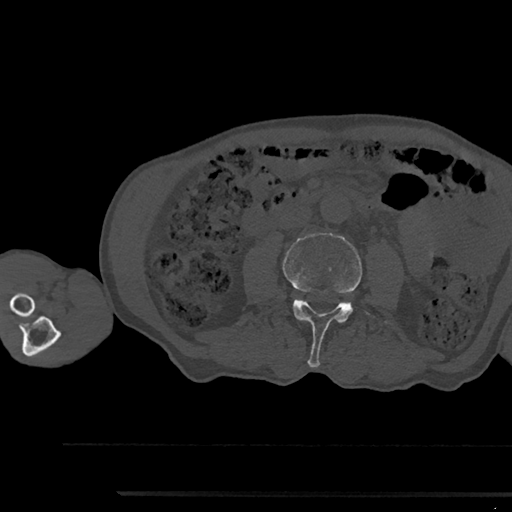
CT including the spine, one axial slice; slice 481 of 797 in the series (ordered by position); reconstruction kernel Br40s/3; 120 kVp; bone window (W 1800 / L 400 HU); 0.5 mm slice thickness; 512 × 512 image matrix. Male patient, age 79 years. From the clinical record (not read from this slice): primary cancer: prostate.
Structures marked on this image (semi-automatic segmentation, software-assisted and operator-edited):
- L3 vertebra: bounding box [x1, y1, x2, y2] px = [282, 233, 362, 367]